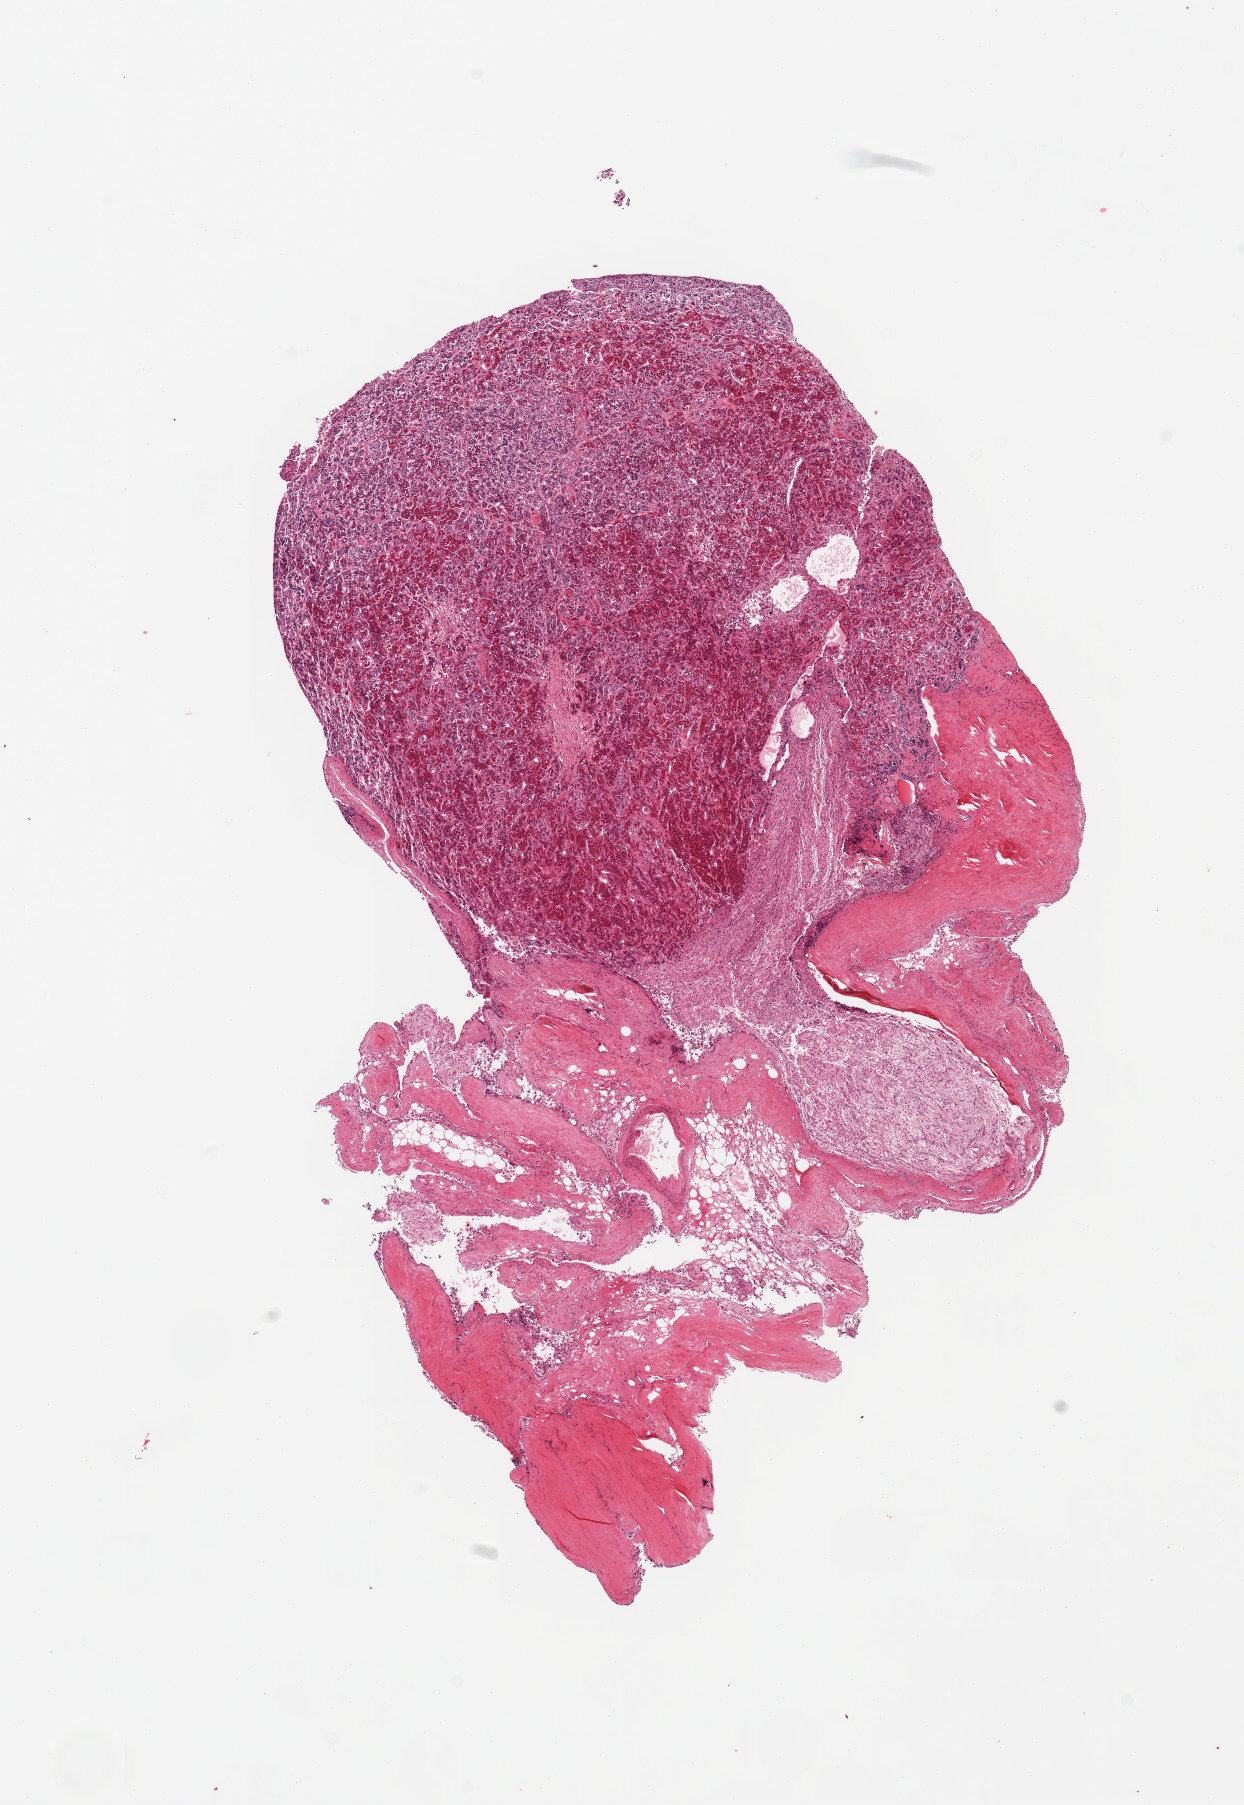
H&E whole-slide image, brightfield — whole scanned area (about 9.8 x 14.3 mm, acquisition: 20x scan) shown as a low-resolution overview. PAXgene-fixed, paraffin-embedded tissue. Sampled site (target tissue): pituitary. Donor tissue sample. Donor: male.
Pathologist's review note for this sample: 1 piece, ~25% neurohypophysis, ~3x3mm; rest is adenohyphphysis, adherent dura.